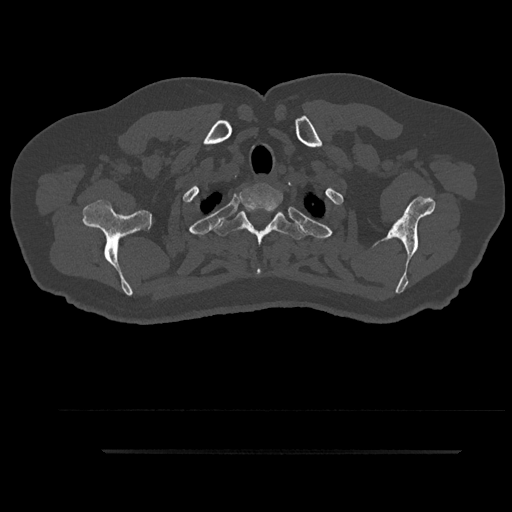
CT including the spine, one axial slice. Position 772 of 797 along the scan axis. Reconstruction kernel Br40s/3. 120 kVp. Bone window (W 1800 / L 400 HU). 512 × 512 image matrix. Male patient, age 63 years. From the clinical record (not read from this slice): primary cancer: renal; vertebrae with lytic lesions (as recorded): T8.
Structures marked on this image (semi-automatic segmentation, software-assisted and operator-edited):
- T1 vertebra: bounding box (x1, y1, x2, y2) in pixels: (239, 185, 283, 219)
- T2 vertebra: (213, 207, 306, 276)